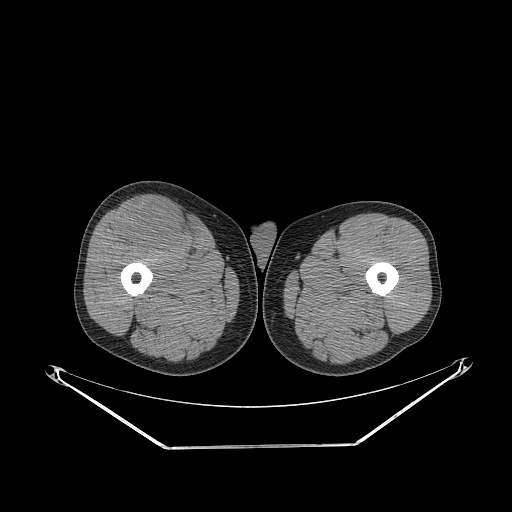
CT of an extremity soft-tissue mass (from a PET/CT study), one axial slice. Position 271 of 311 along the scan axis. Soft-tissue window (W 400 / L 40 HU). 3.75 mm slice thickness. 512 × 512 image matrix. Male patient. Case-level facts recorded for this patient, not image findings: histological type: pleiomorphic leiomyosarcoma; grade: intermediate; site of the primary tumour: right thigh.
Outlined on this slice (expert contour drawn on MRI and transferred to this co-registered scan by the dataset authors):
- gross tumour volume including surrounding oedema: bounding box (x1, y1, x2, y2) in pixels: (119, 203, 186, 252)
- gross tumour volume (mass): (119, 203, 186, 252)